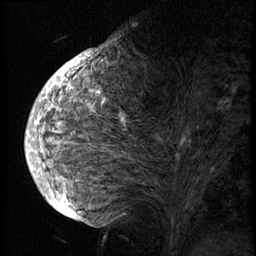
Breast MRI (dynamic contrast-enhanced), one sagittal slice. Position 34 of 74 along the scan axis. 3 images stored at this slice position (order not interpretable as contrast timing). 1.5 T. TE 4.2 ms, TR 8.9 ms. 256 × 256 image matrix, field of view 200 × 200 mm. Female patient, age 57 years. Case-level facts recorded for this patient, not image findings: setting: breast cancer imaged before/during neoadjuvant chemotherapy; receptor status: HER2-positive.
Structures marked on this image (semi-automatic segmentation, software-assisted and operator-edited):
- analysis volume of interest (the breast-tissue region the enhancement analysis was run in; not a lesion): bounding box [x1, y1, x2, y2] px = [40, 62, 237, 175]
- tumour enhancement mask (voxels above the 140 % enhancement threshold inside the analysis volume of interest): [40, 64, 183, 172]